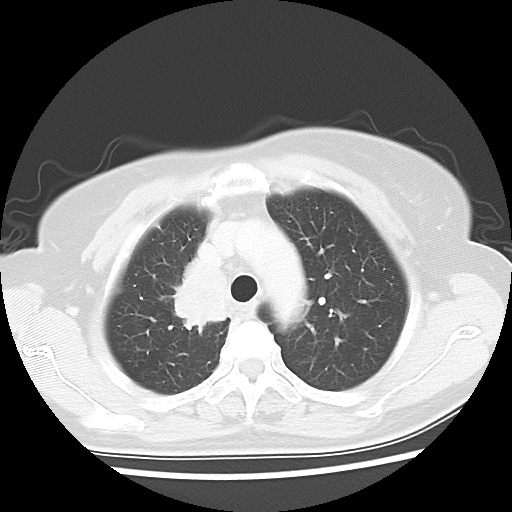
Chest CT, one axial slice; slice 44 of 56 in the series (ordered by position); lung window (W 1500 / L -600 HU); 5 mm slice thickness; 512 × 512 image matrix, field of view 314 × 314 mm. Patient: female, 62 years. Case-level facts recorded for this patient, not image findings: clinical TNM (as recorded): T2 N1 M1a.
Annotated regions visible in this slice (rectangle marked by the reading radiologist):
- lung tumour (recorded histology: adenocarcinoma): bounding box [x1, y1, x2, y2] px = [156, 245, 235, 329]